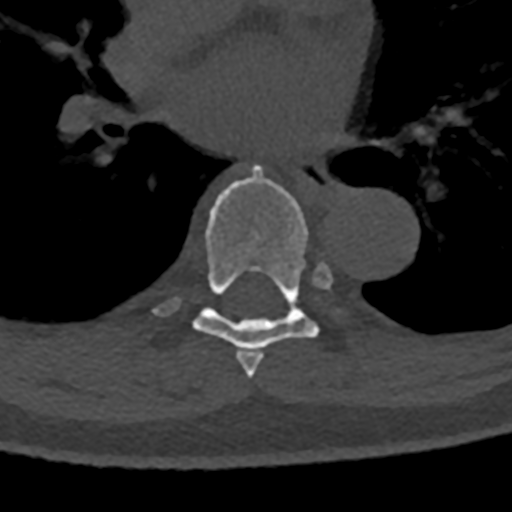
CT including the spine, one axial slice. Position 763 of 797 along the scan axis. Reconstruction kernel Br40s/3. Bone window (W 1800 / L 400 HU). 512 × 512 image matrix, field of view 160 × 160 mm. Patient: male, 74 years. Case-level facts recorded for this patient, not image findings: primary cancer: renal; vertebrae with lytic lesions (as recorded): T10, L1, L2, L3, L4, L5.
Annotated regions visible in this slice (semi-automatically segmented with operator editing):
- T6 vertebra: bounding box (x1, y1, x2, y2) in pixels: (245, 353, 263, 378)
- T7 vertebra: (151, 165, 345, 369)